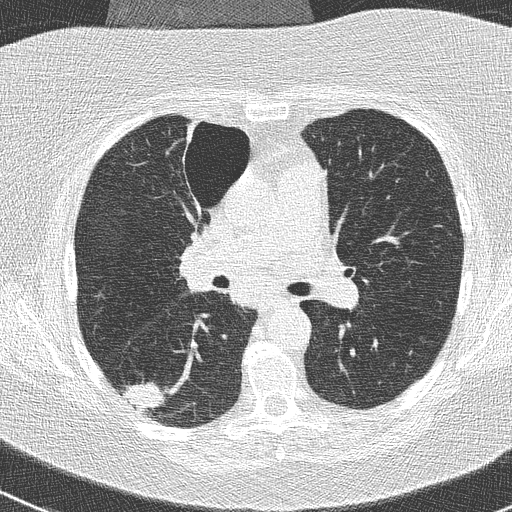
Low-dose screening chest CT, one axial slice; slice 154 of 261 in the series (ordered by position); reconstruction kernel B50f; 120 kVp; lung window (W 1500 / L -600 HU); 512 × 512 image matrix, field of view 310 × 310 mm.
Annotated regions visible in this slice (manually delineated by an expert):
- lesion 1 (tumor, lower lobe of right lung): box from (x=123, y=382) to (x=165, y=414) px